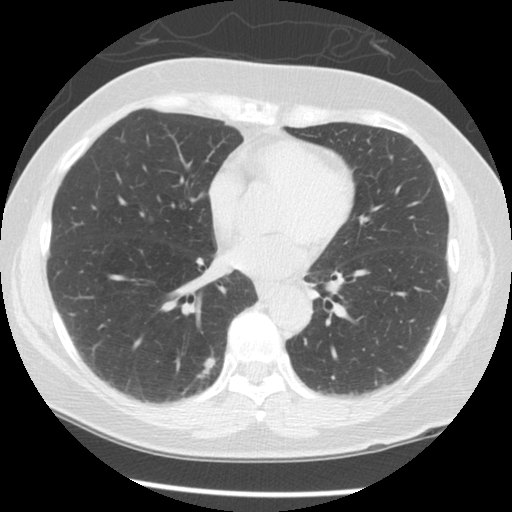
Low-dose screening chest CT, one axial slice. Slice 58 of 125 in the series (ordered by position). Reconstruction kernel STANDARD. 120 kVp. Lung window (W 1500 / L -600 HU). 2.5 mm slice thickness. 512 × 512 image matrix, field of view 331 × 331 mm.
Outlined on this slice (manually delineated by an expert):
- lesion 1 (tumor, lower lobe of right lung): bounding box [x1, y1, x2, y2] px = [197, 353, 216, 379]